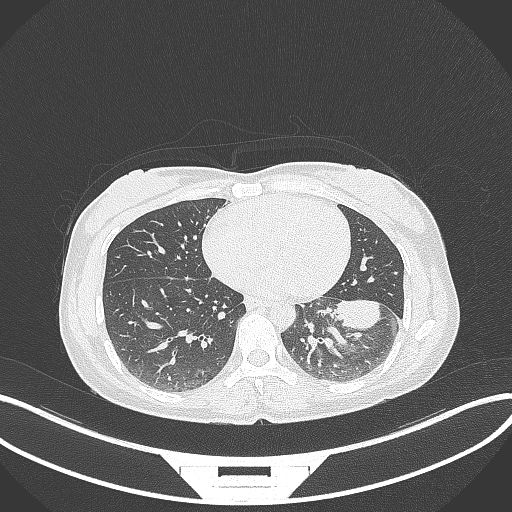
Chest CT, one axial slice. Slice 23 of 244 in the series (ordered by position). 120 kVp. Lung window (W 1500 / L -600 HU). 512 × 512 image matrix, field of view 400 × 400 mm. Female patient, age 41 years. From the clinical record (not read from this slice): clinical TNM (as recorded): T2a N3 M1b.
Outlined on this slice (bounding box drawn by a radiologist):
- lung tumour (recorded histology: adenocarcinoma): bounding box [x1, y1, x2, y2] px = [332, 297, 390, 339]